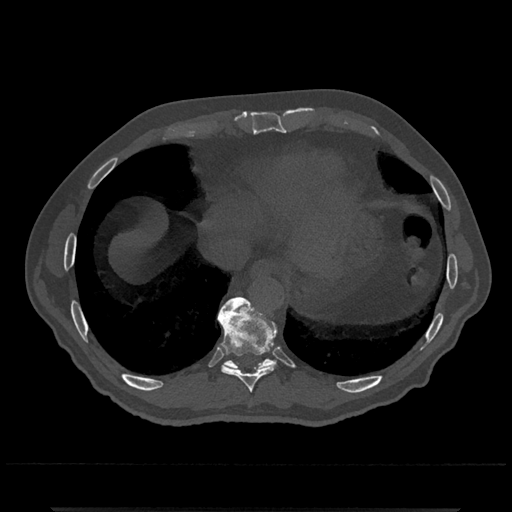
CT including the spine, one axial slice; slice 594 of 797 in the series (ordered by position); reconstruction kernel Br40s/3; bone window (W 1800 / L 400 HU); 0.5 mm slice thickness; 512 × 512 image matrix. Patient: male, 67 years. Case-level facts recorded for this patient, not image findings: primary cancer: prostate.
Annotated regions visible in this slice (semi-automatic segmentation, software-assisted and operator-edited):
- T10 vertebra: box from (x=218, y=297) to (x=276, y=369) px
- T9 vertebra: (x=217, y=298)–(x=278, y=393)